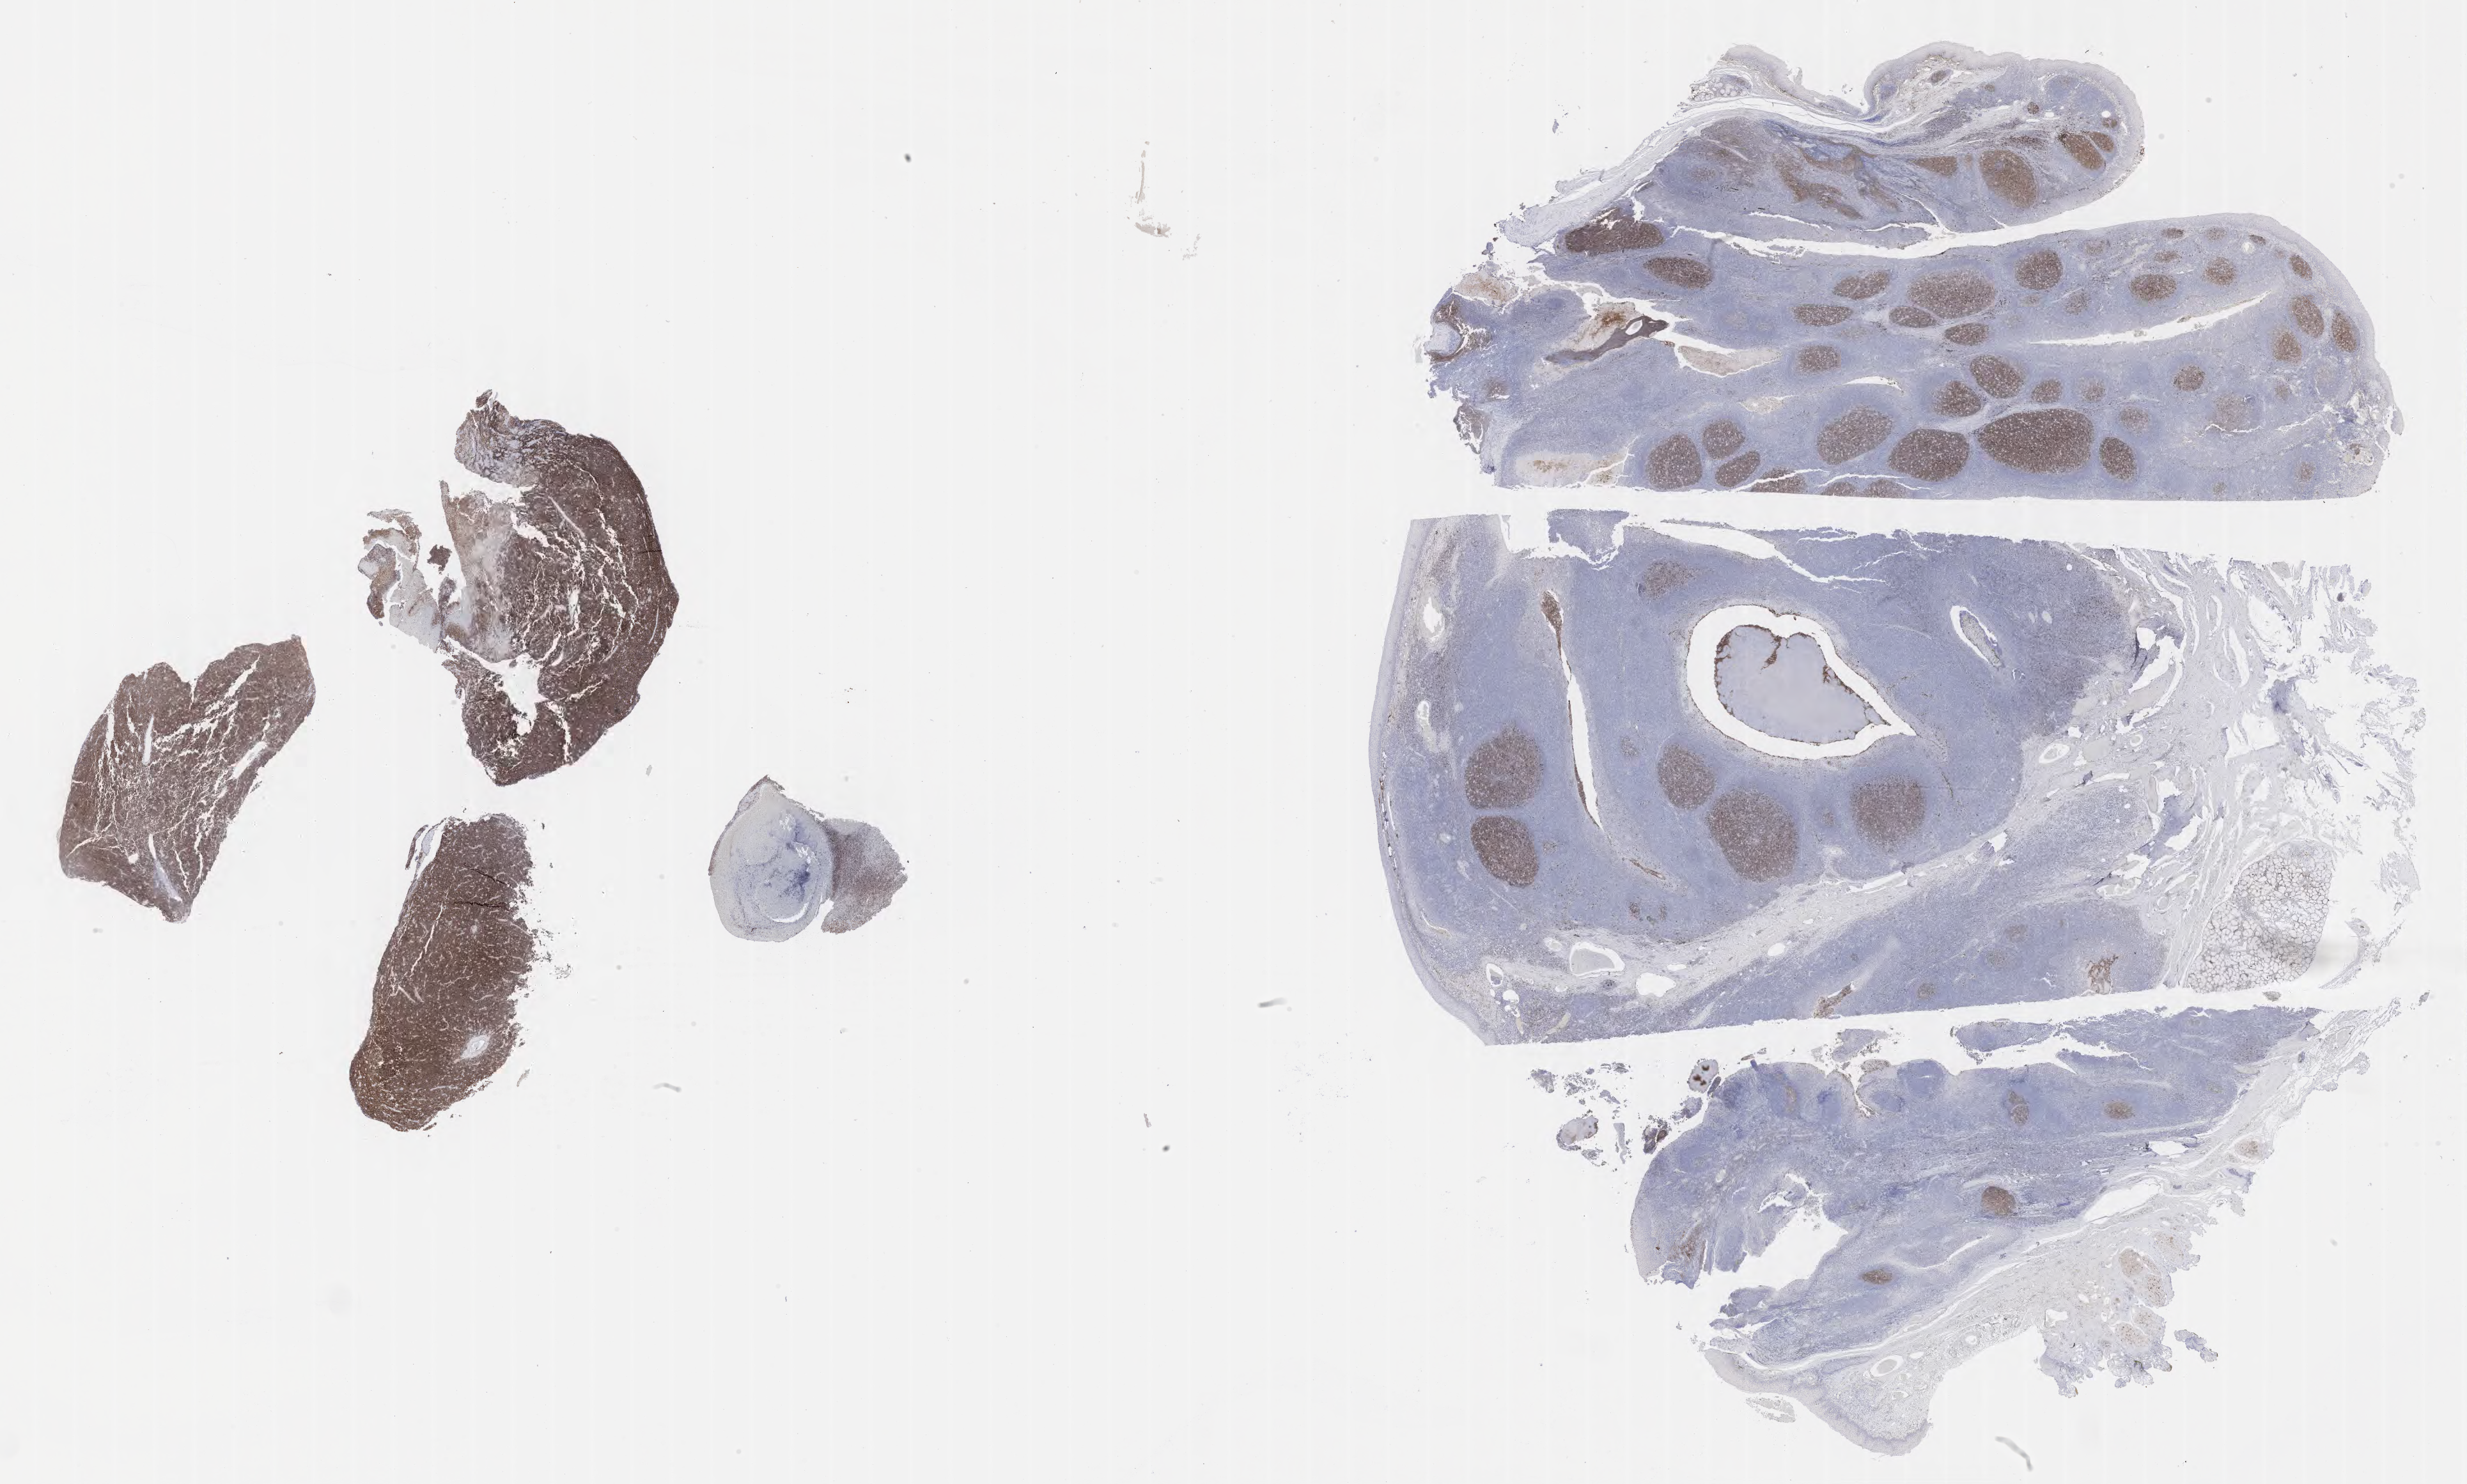
Whole-slide image, immunohistochemical stain for CD10, low-resolution overview of the scanned area, about 31.2 x 18.8 mm; tumor tissue. Male patient, age 10 years.
* histologic diagnosis: Burkitt lymphoma, NOS